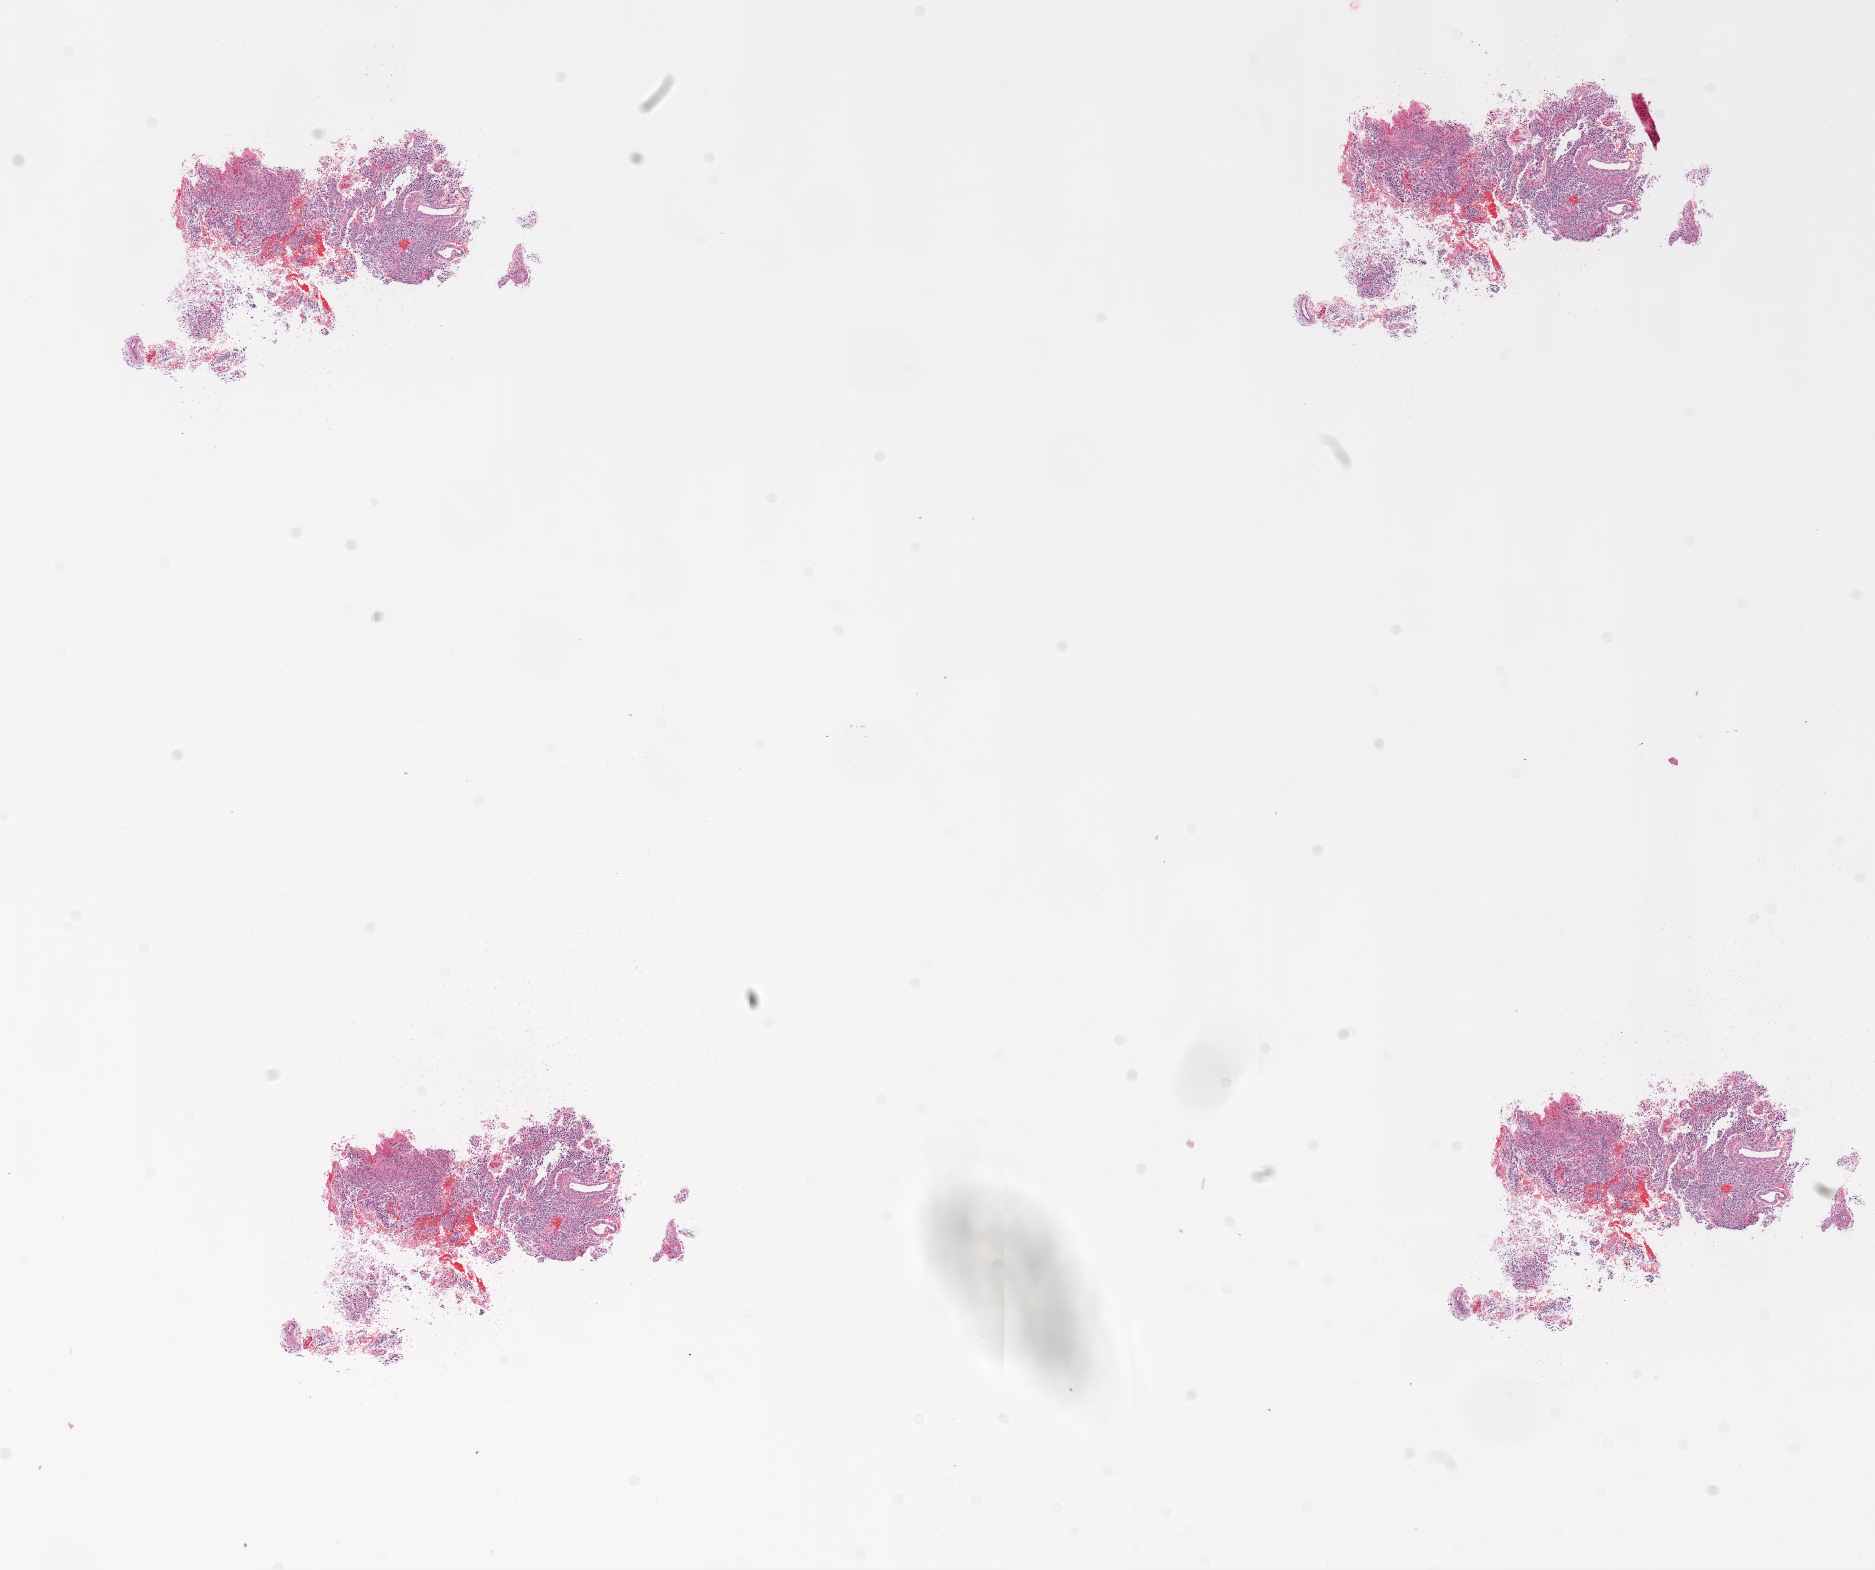
Hematoxylin and eosin (H&E) stained whole-slide image, shown as a low-resolution overview of the whole scanned area (about 15.0 x 12.6 mm, from a 20x scan), formalin-fixed paraffin-embedded (FFPE) diagnostic section, primary tumour sample from the brain. Patient: male, age at initial diagnosis 53 years.
Pathologic diagnosis: Glioblastoma.